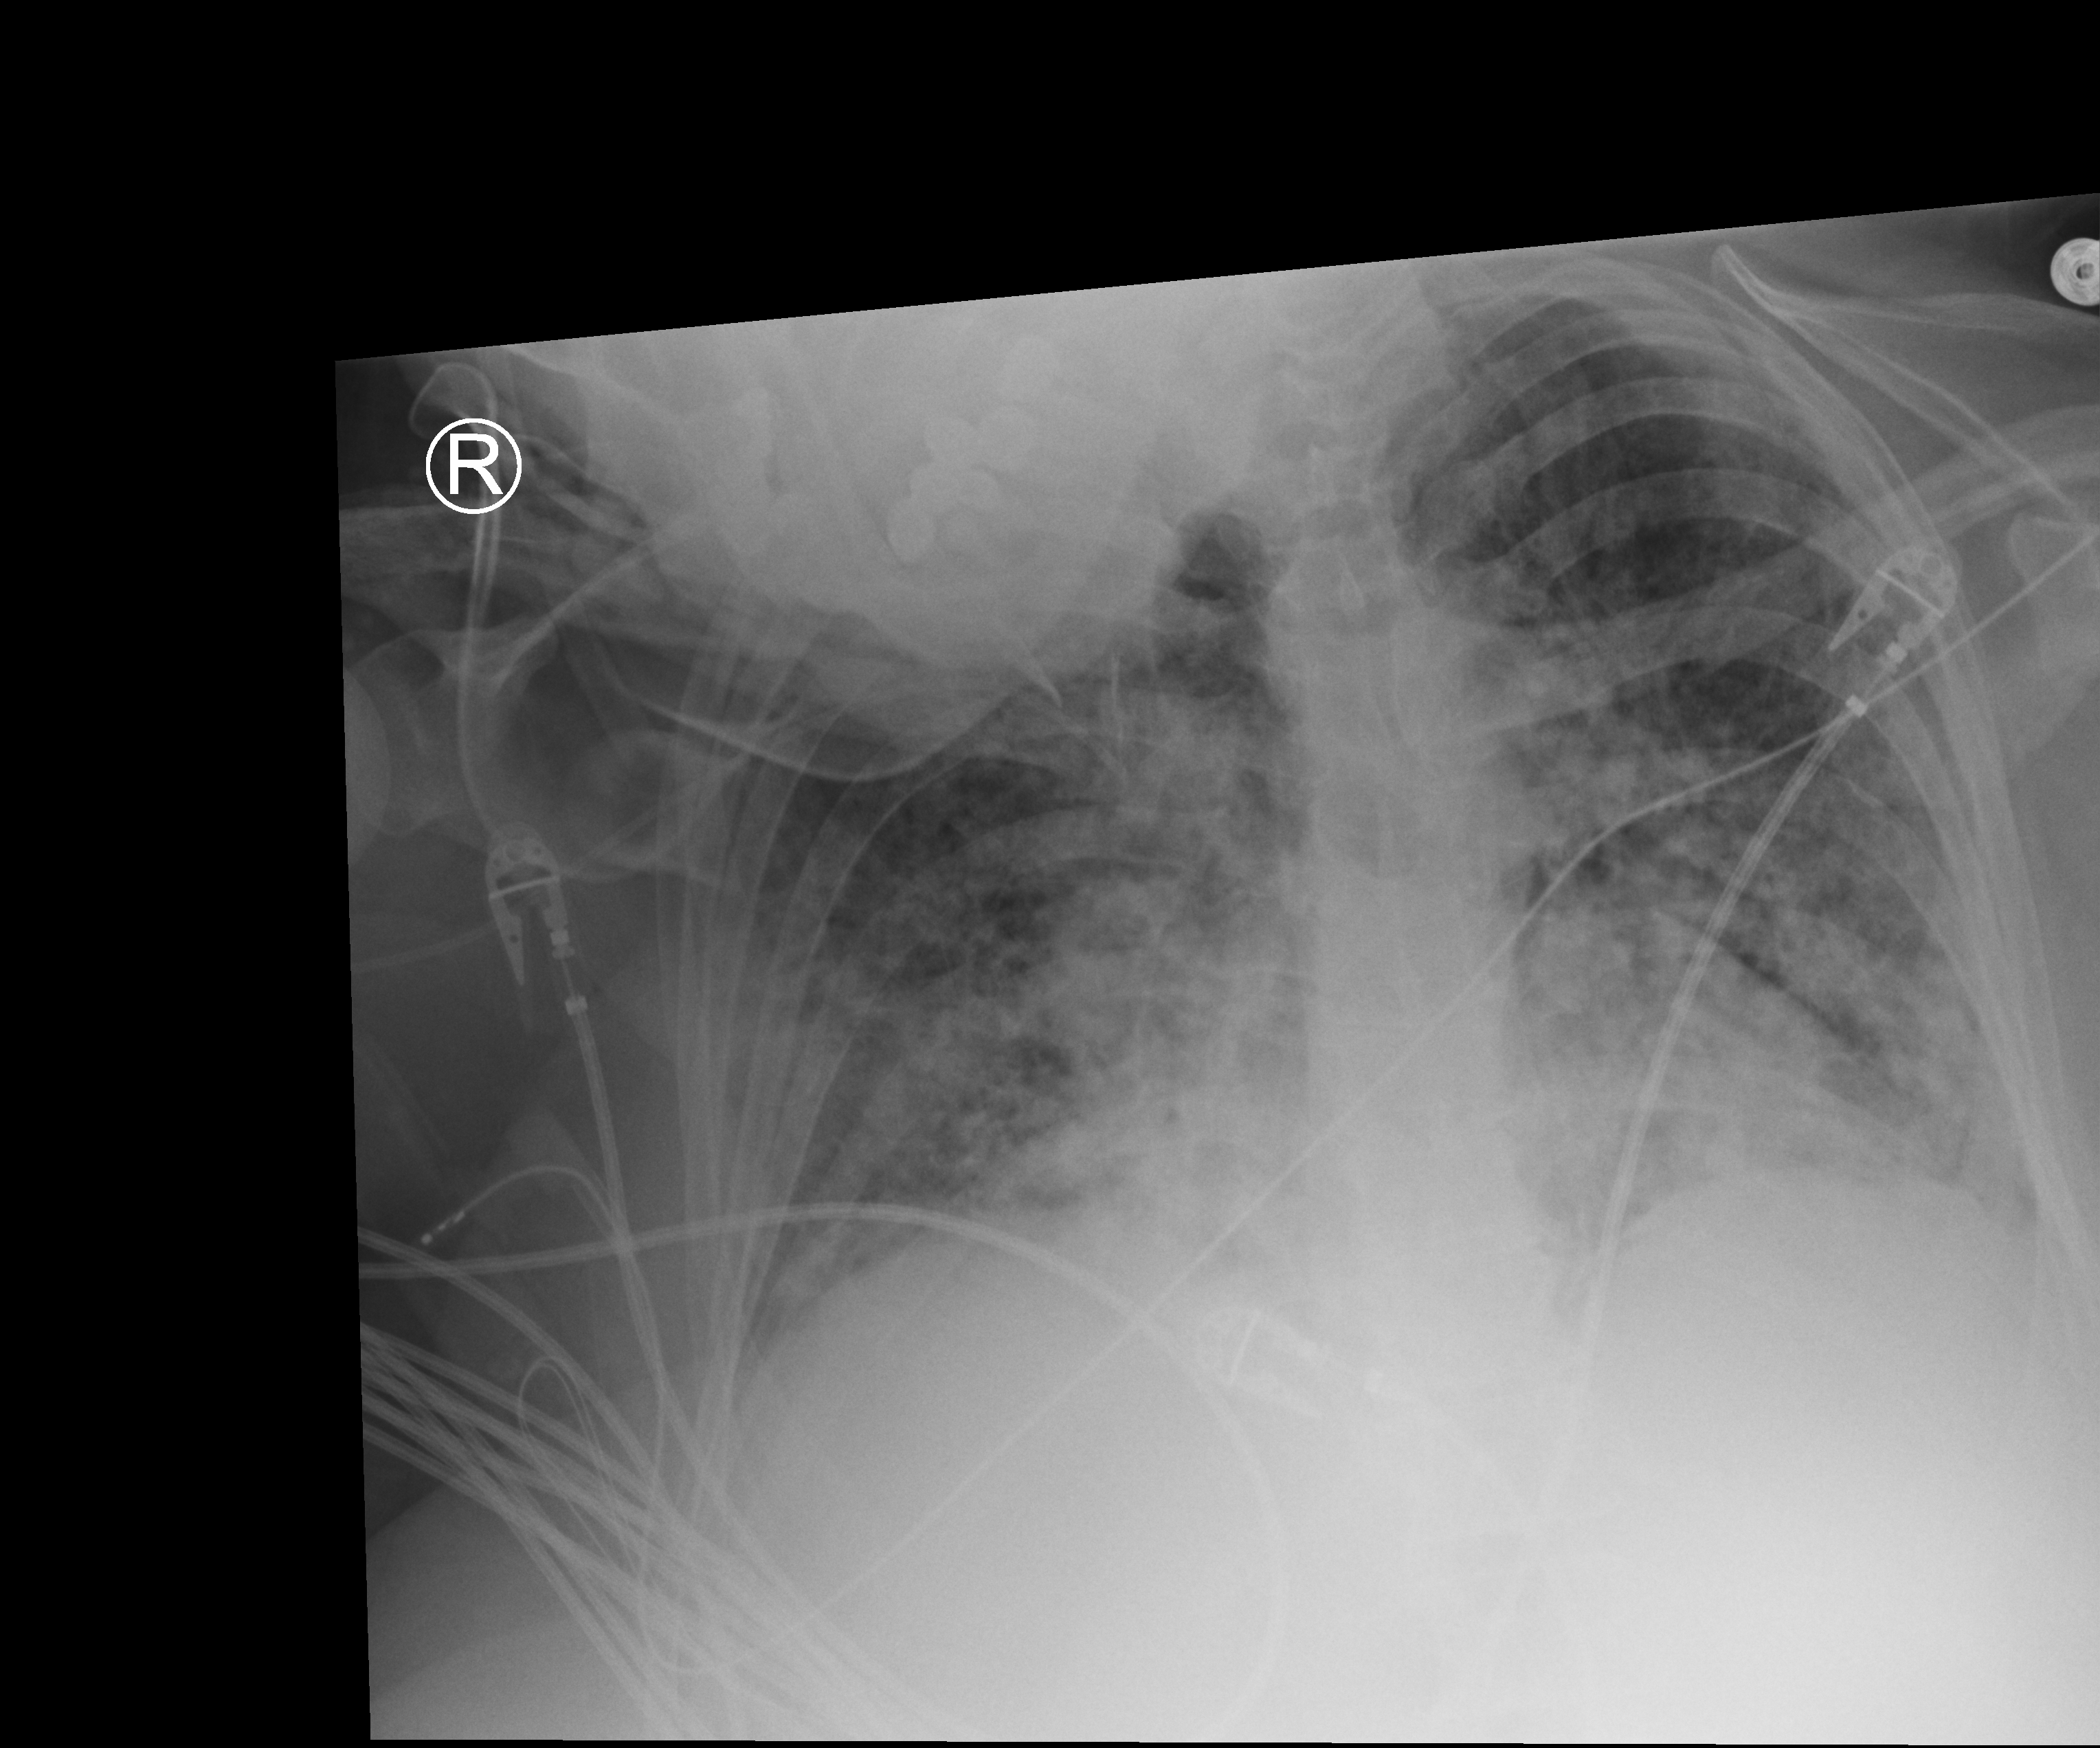
Bedside chest radiograph (computed radiography), anteroposterior (AP) projection. Patient hospitalised with COVID-19; female, aged 60–74 years.
From the hospital-stay record, not from the radiograph (when in the stay this image was taken is not recorded): smoking status (admission record): never.